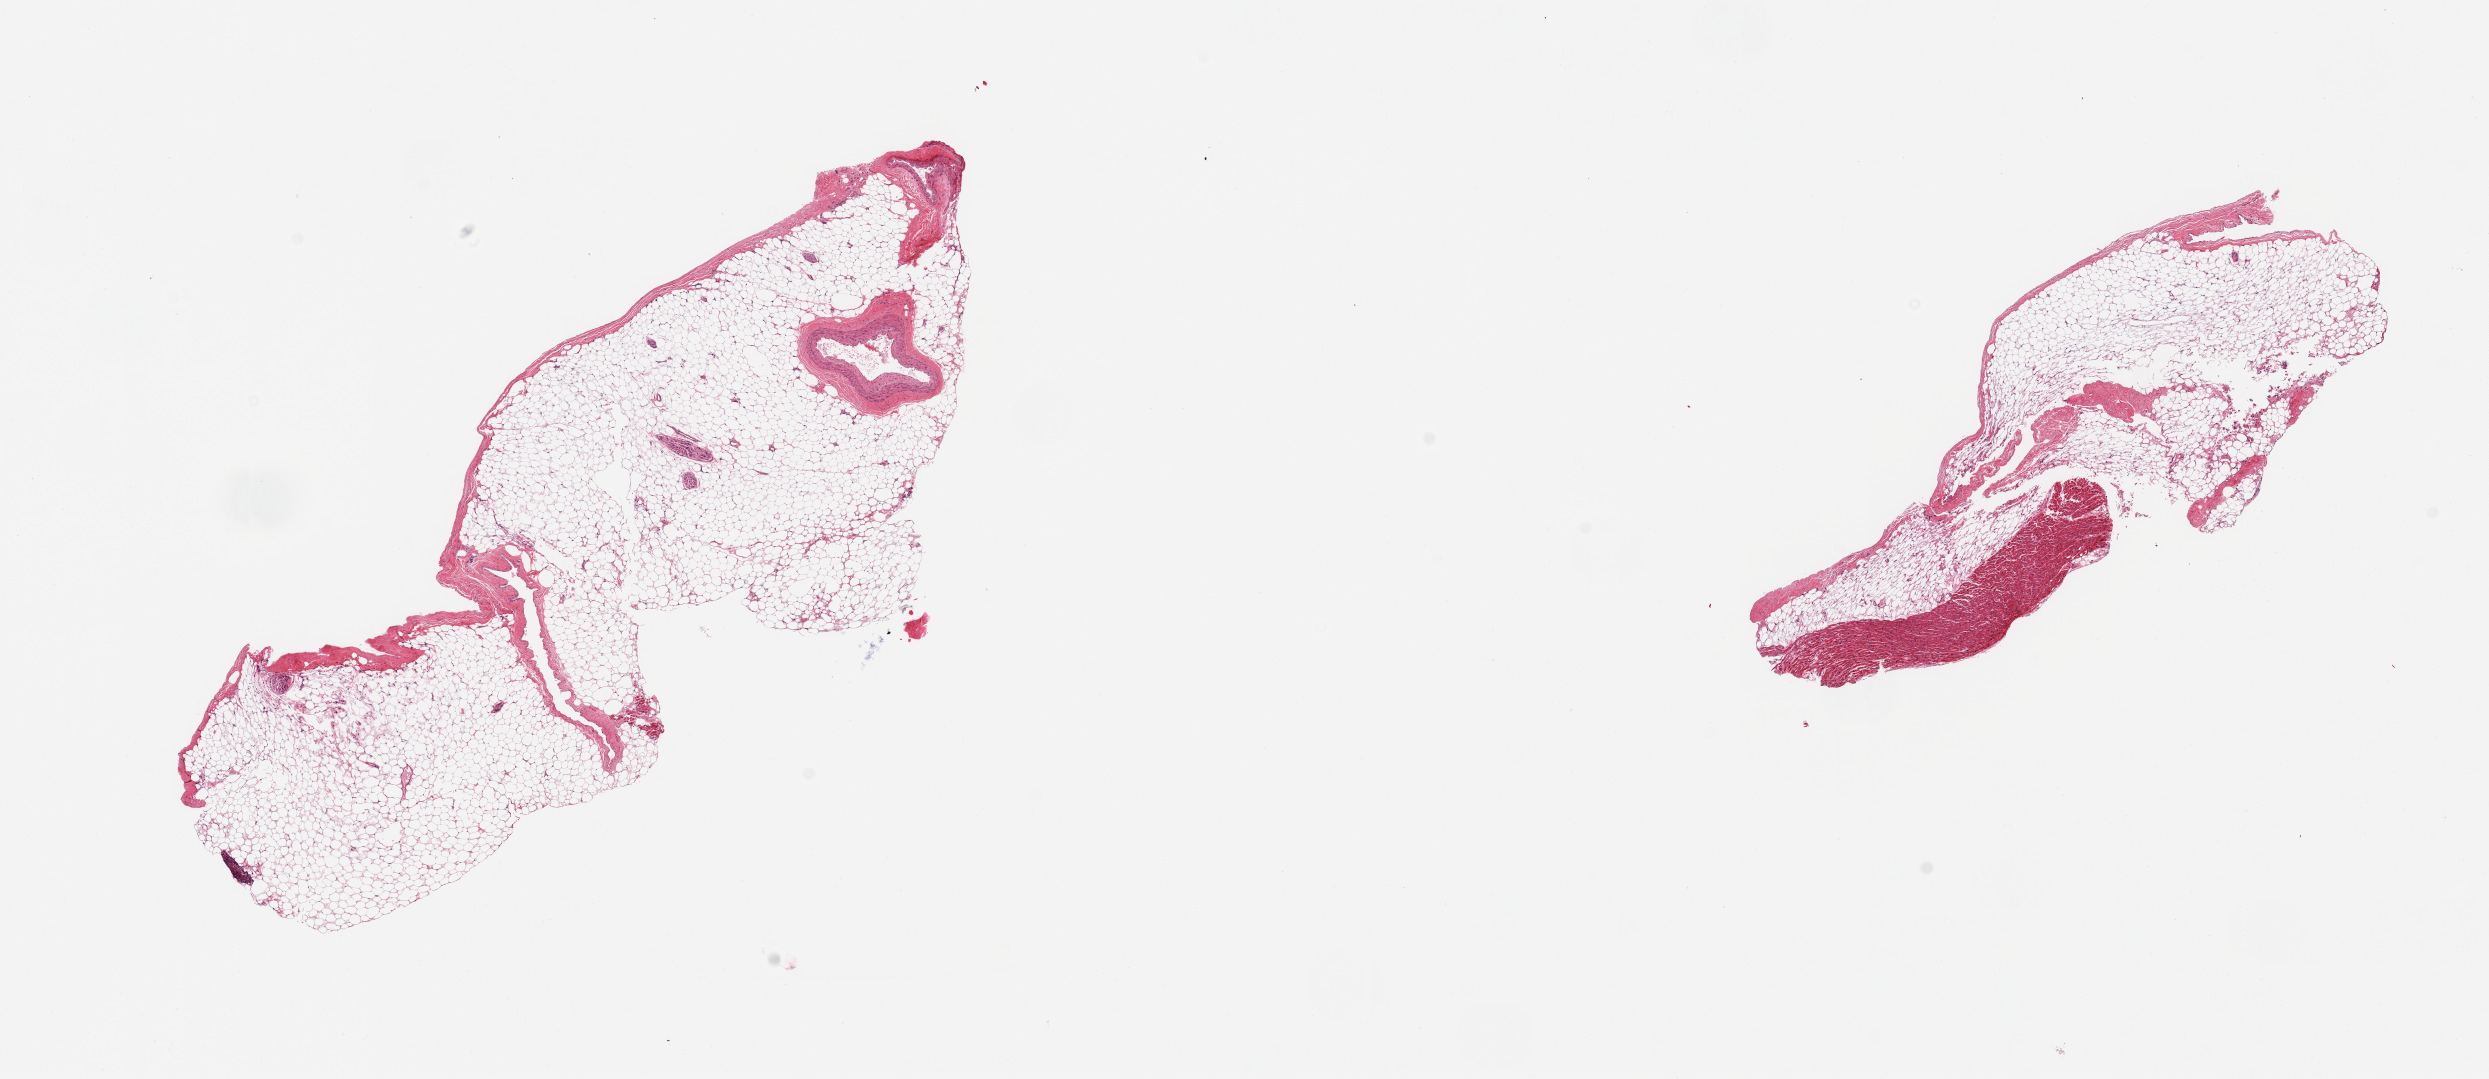
Haematoxylin and eosin whole-slide image — low-resolution overview of the scanned area, about 19.7 x 8.5 mm. PAXgene-fixed paraffin-embedded (PFPE) section. Sampled site (target tissue): coronary artery. Donor tissue sample. Donor: female.
Review note (as recorded): 2 pieces; predominantly fat and portion of myocardium, minimal artery (<10%).